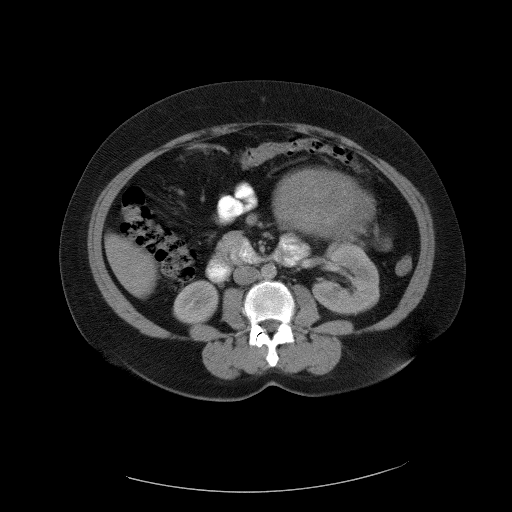
Contrast-enhanced abdominal CT, one axial slice. Position 53 of 90 along the scan axis. 120 kVp. Intravenous contrast given. Soft-tissue window (W 400 / L 40 HU). 5 mm slice thickness. 512 × 512 image matrix. Patient: female, 55 years. From the clinical record (not read from this slice): diagnosis: adrenocortical carcinoma; tumour side: left adrenal; tumour size at pathology: 22 cm; Ki-67 index: 10 %; stage (as recorded): 3.
Structures marked on this image (semi-automatic segmentation, software-assisted and operator-edited):
- mass: bounding box [x1, y1, x2, y2] px = [276, 170, 375, 242]